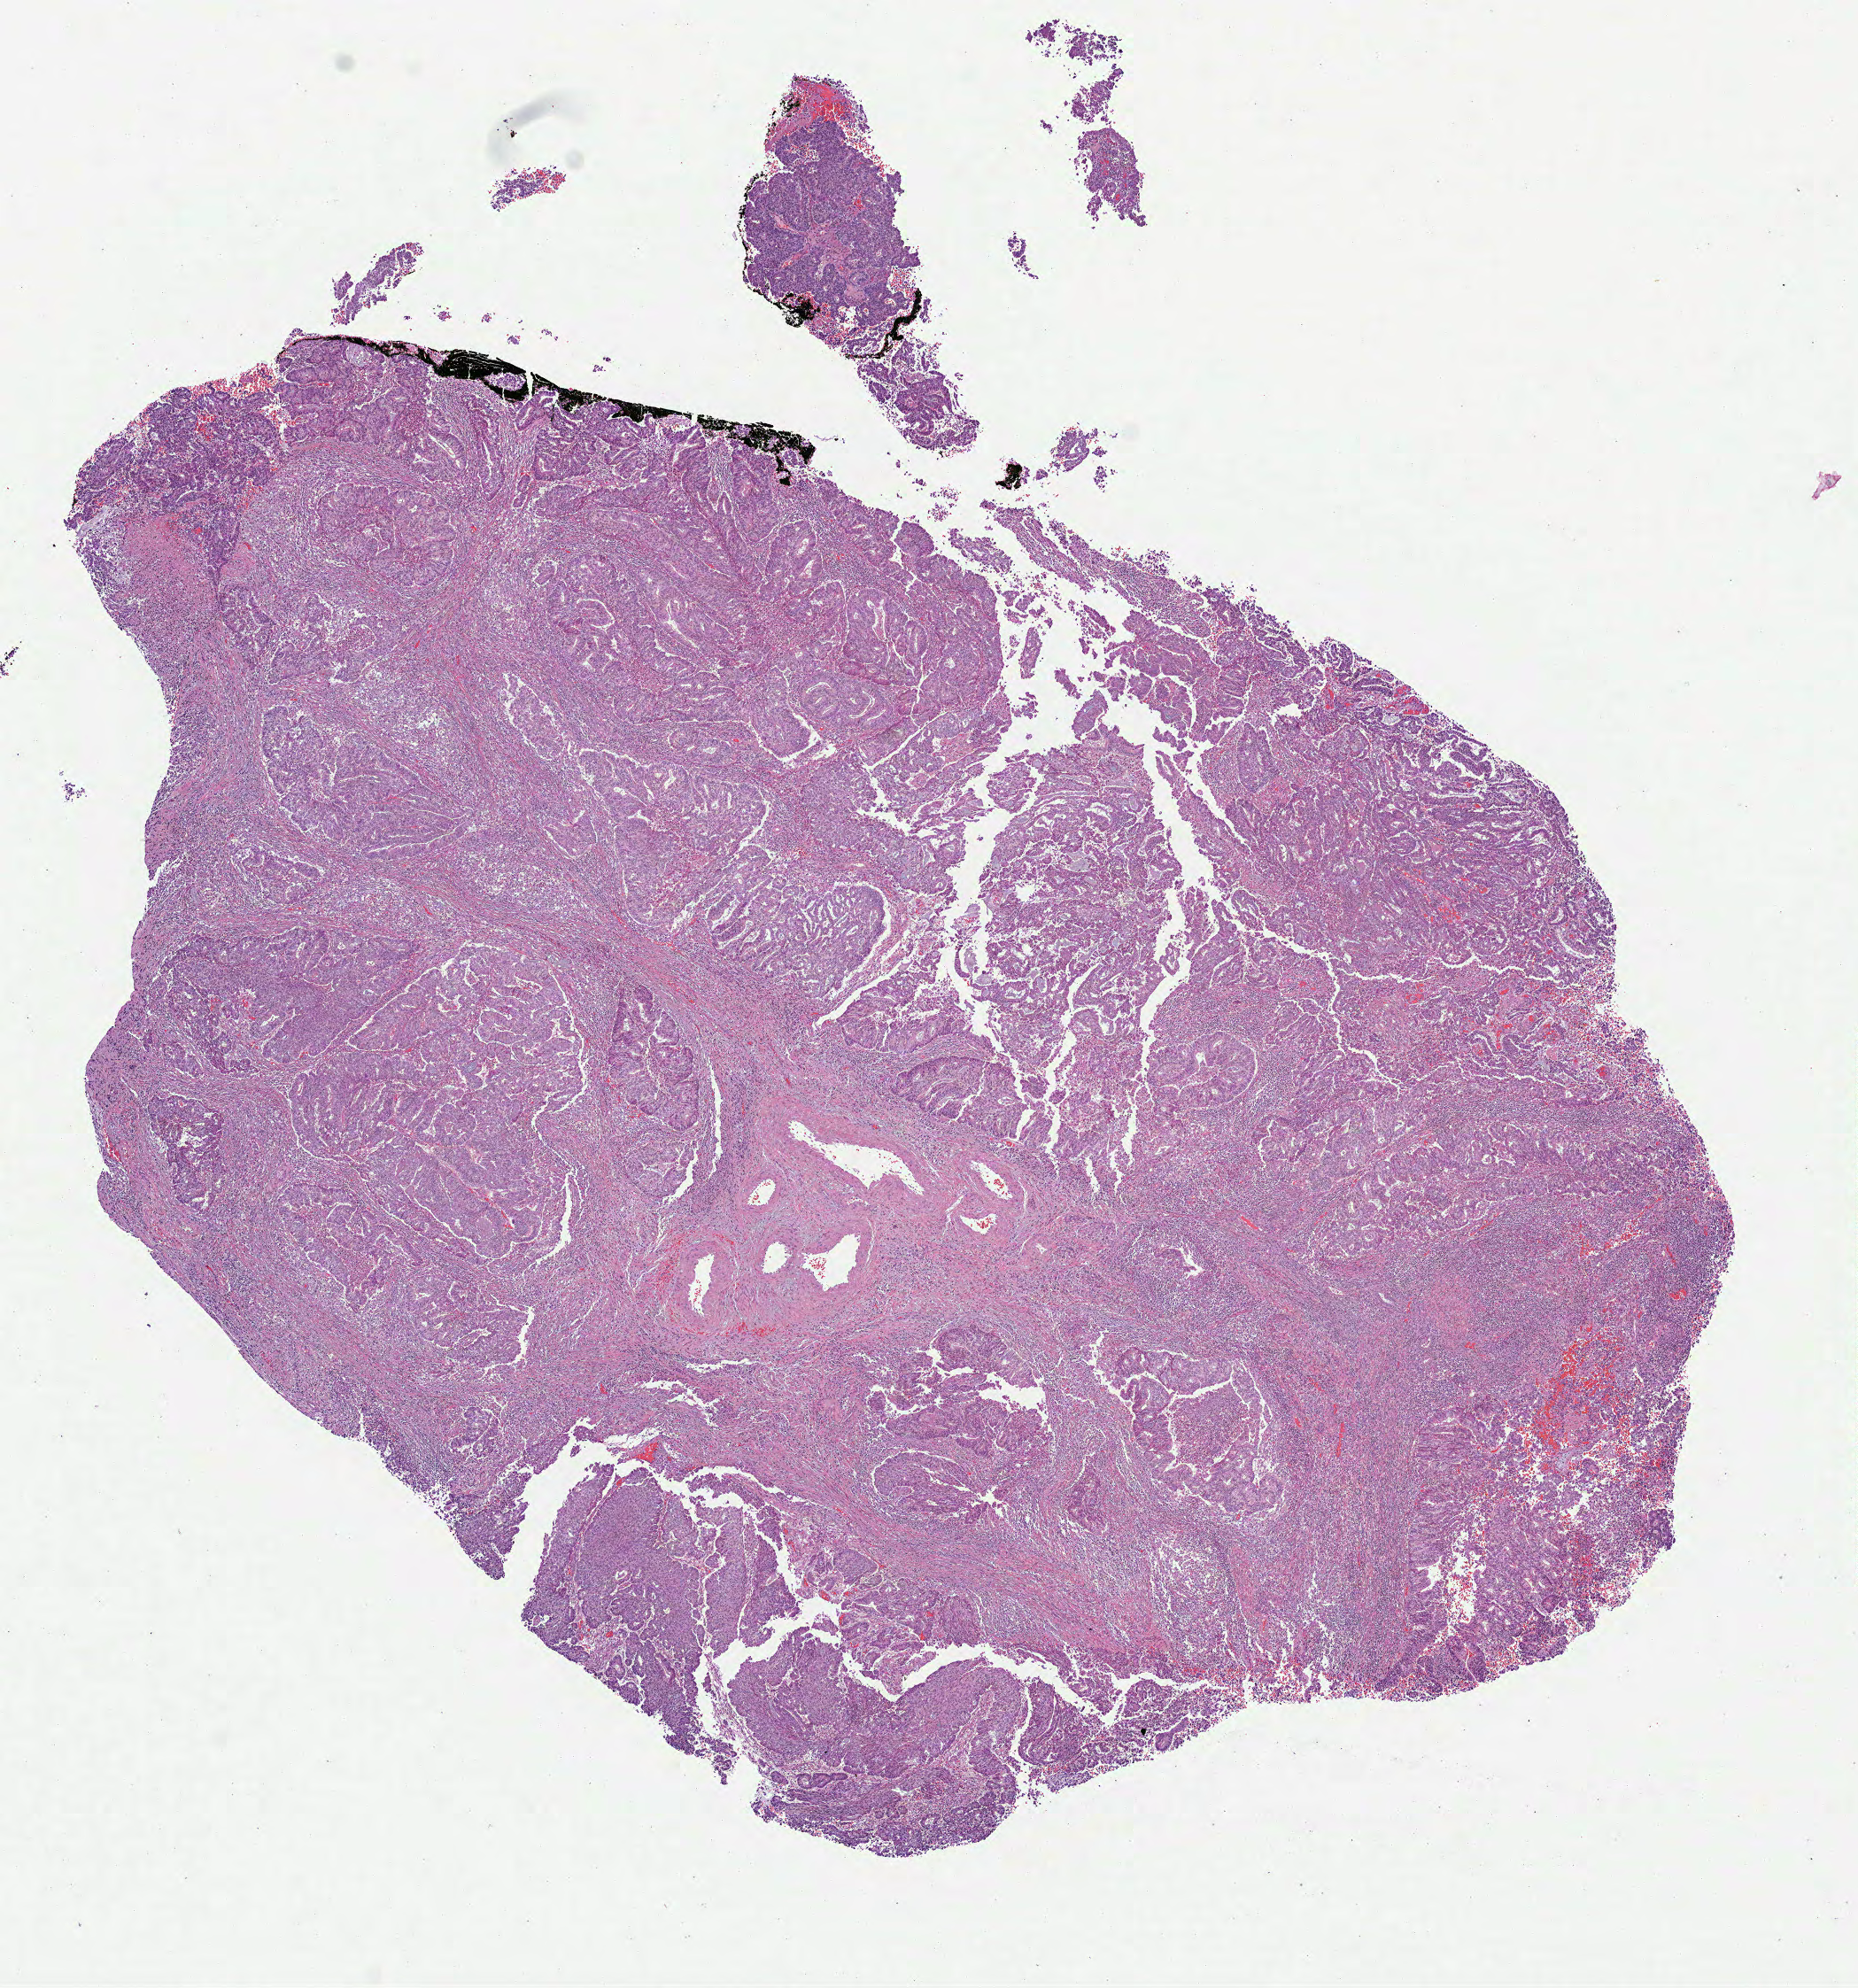
Digitized H&E tissue section (whole slide), a low-resolution overview of the entire scanned area, about 8.5 x 9.1 mm, formalin-fixed paraffin-embedded (FFPE) diagnostic section, primary tumour sample from the uterus. Female patient; age at initial diagnosis 53 years. Histologic grade: G3 (poorly differentiated).
- pathologic diagnosis: Serous cystadenocarcinoma, NOS
- FIGO stage: IA